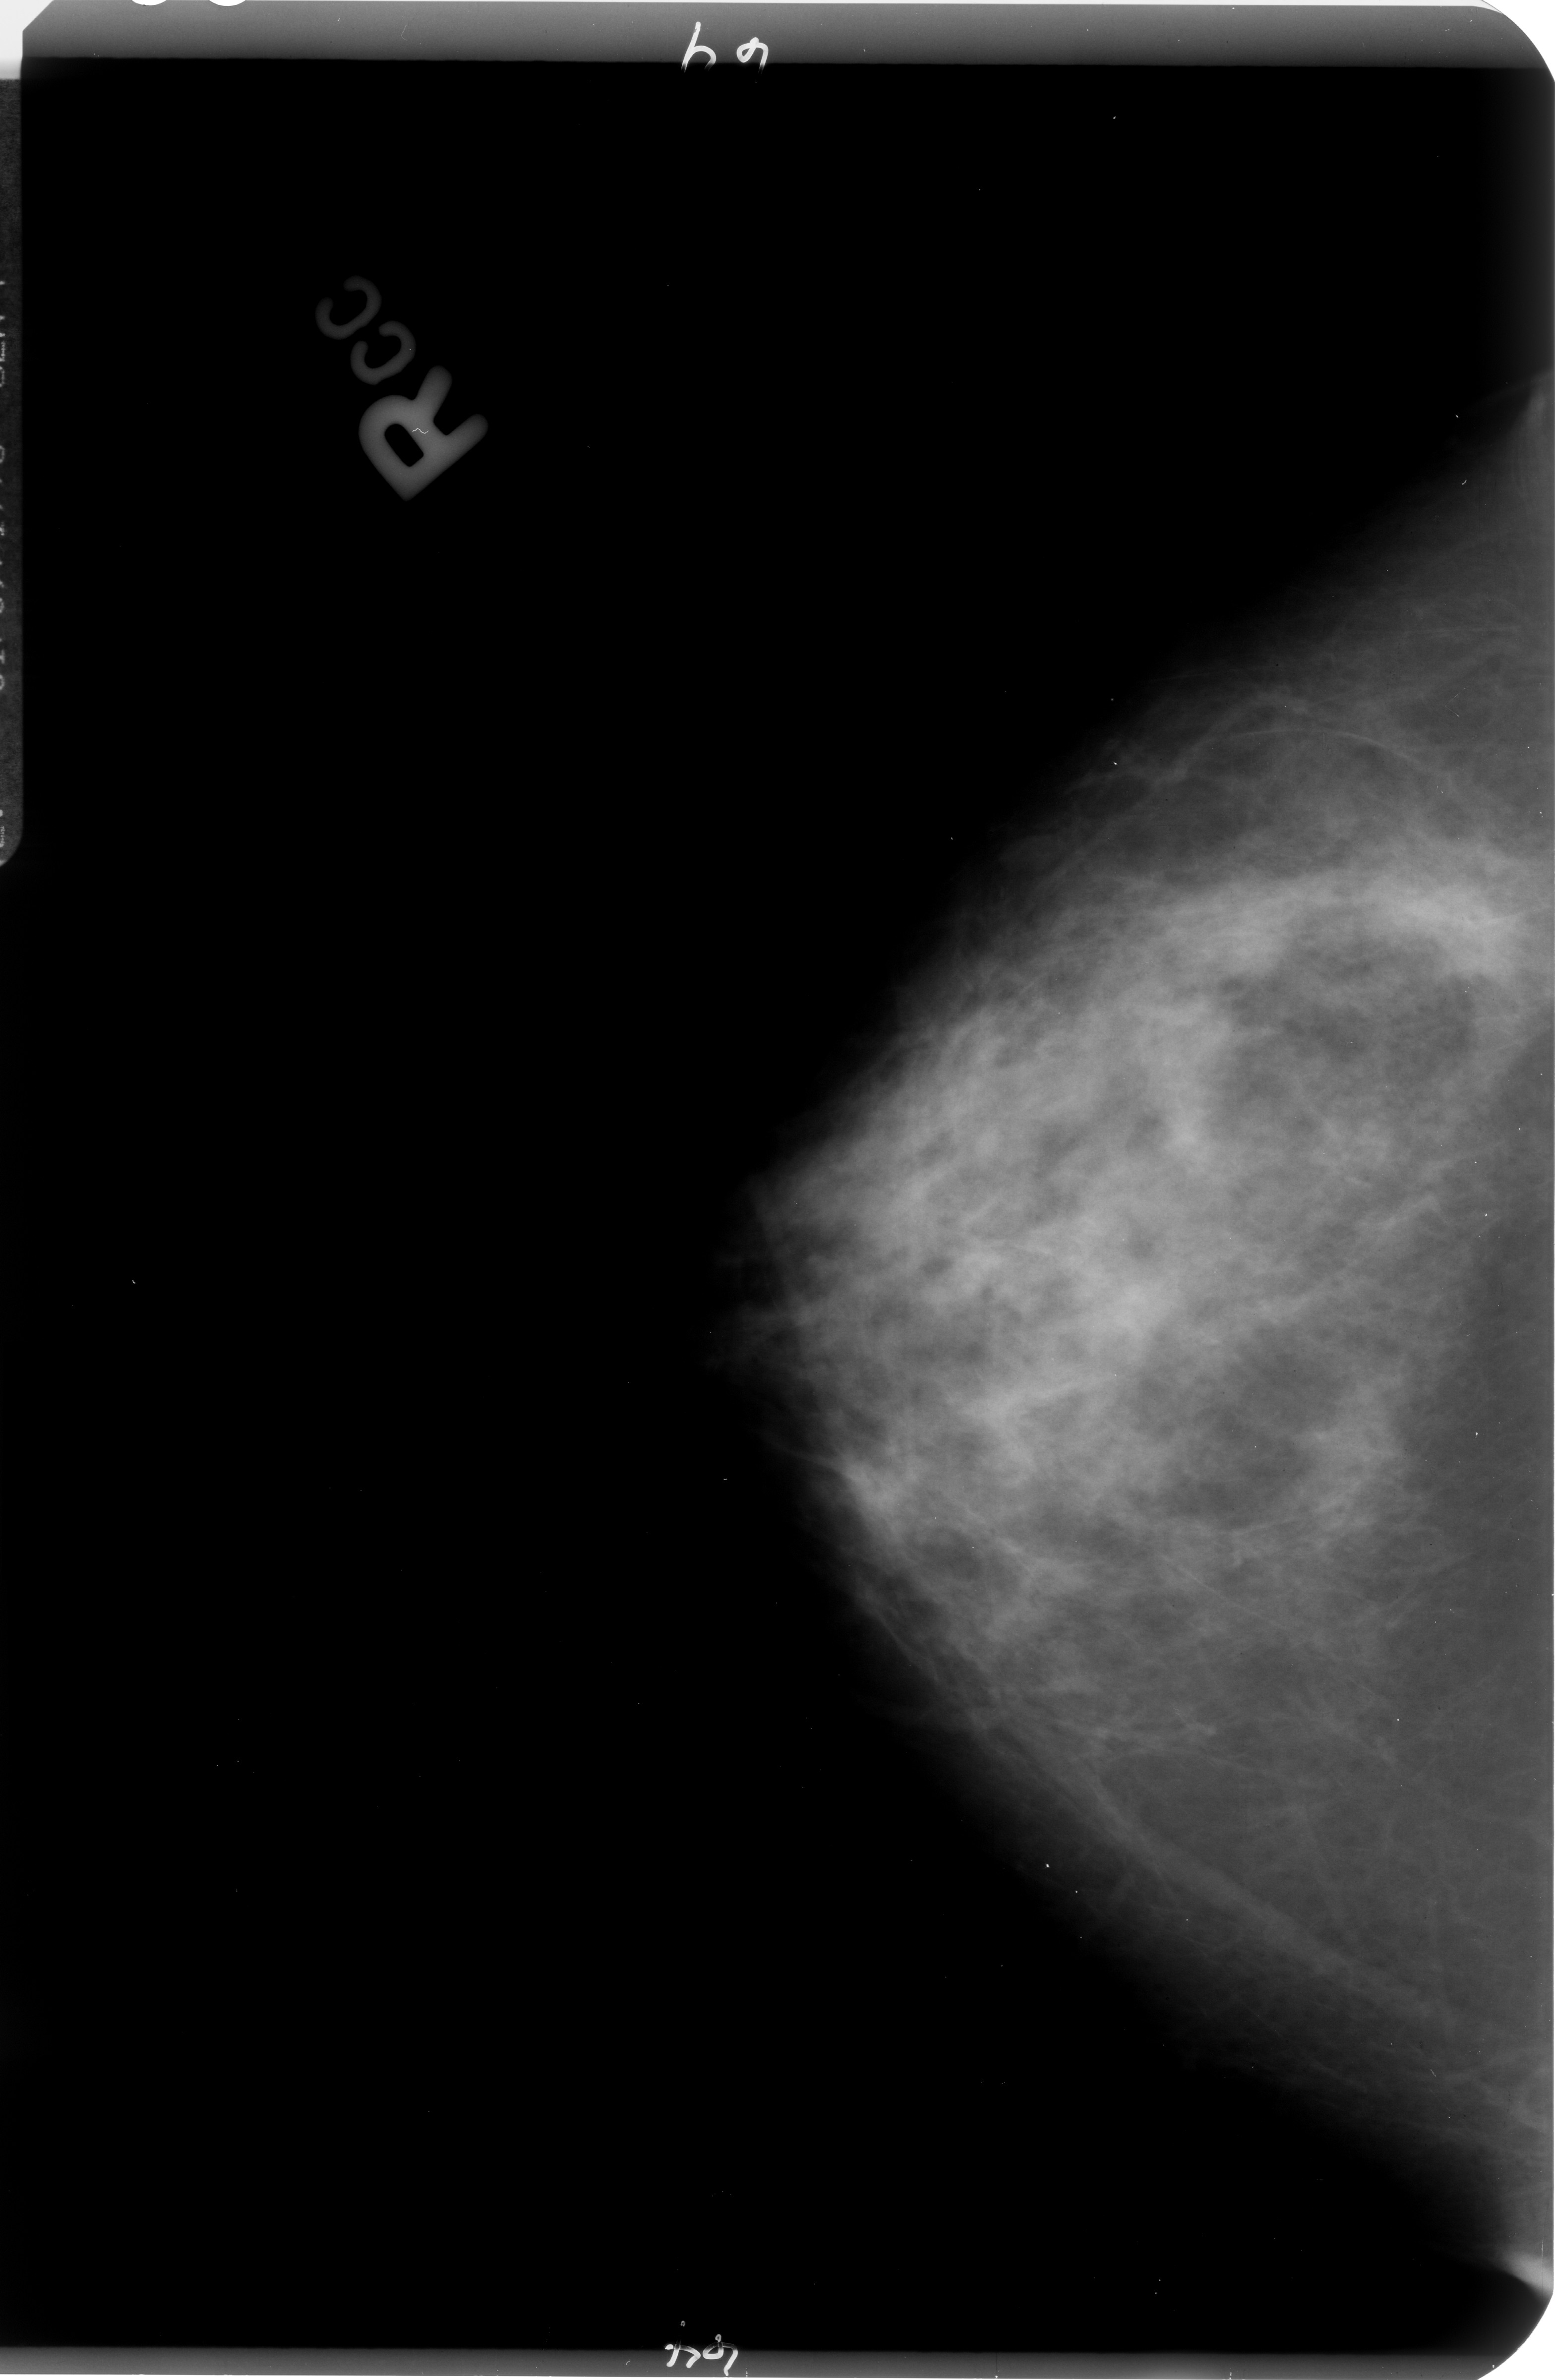
Mammogram (digitized film), right breast, craniocaudal (CC) view, breast composition: heterogeneously dense (BI-RADS density category 3 of 4).
Abnormality record for this image: mass, shape architectural distortion, margins ill defined; BI-RADS assessment category 4; pathology (as recorded): malignant.